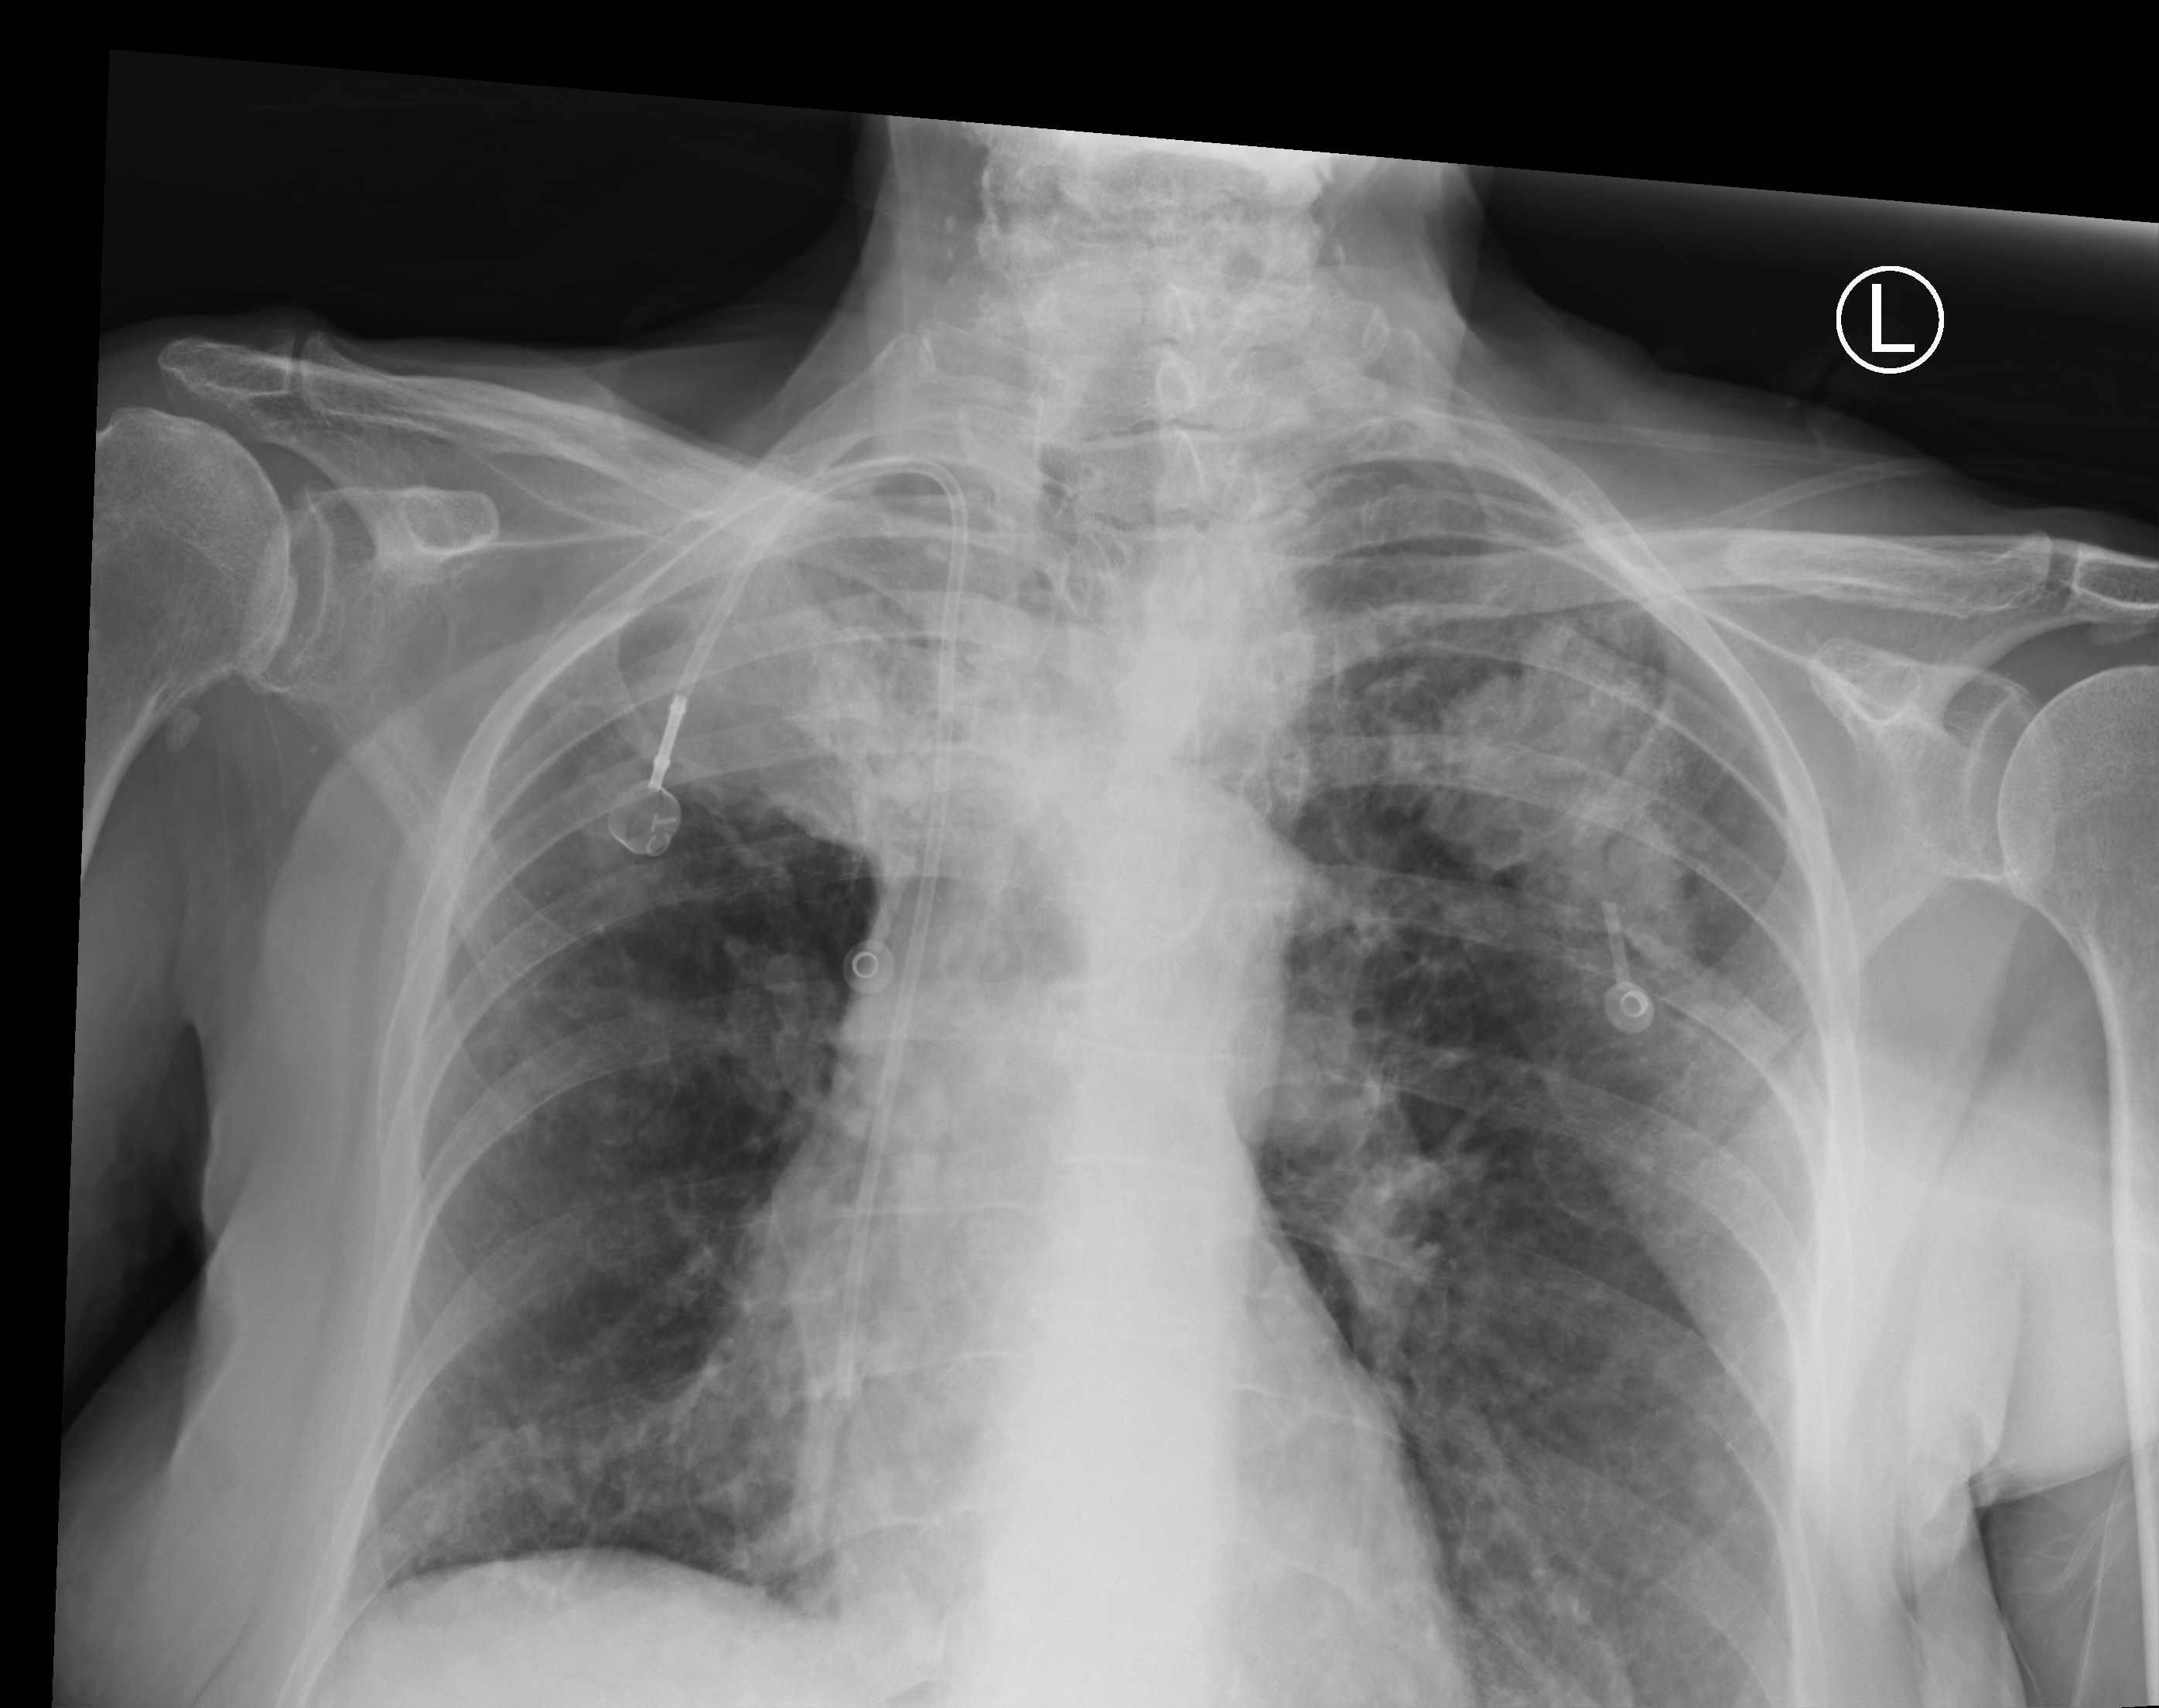
Chest X-ray (portable). Female patient hospitalised with COVID-19, age 60–74 years.
Admission-level facts for this patient (not findings on this image; timing relative to this image not recorded):
- admitted to intensive care during this hospital stay: no